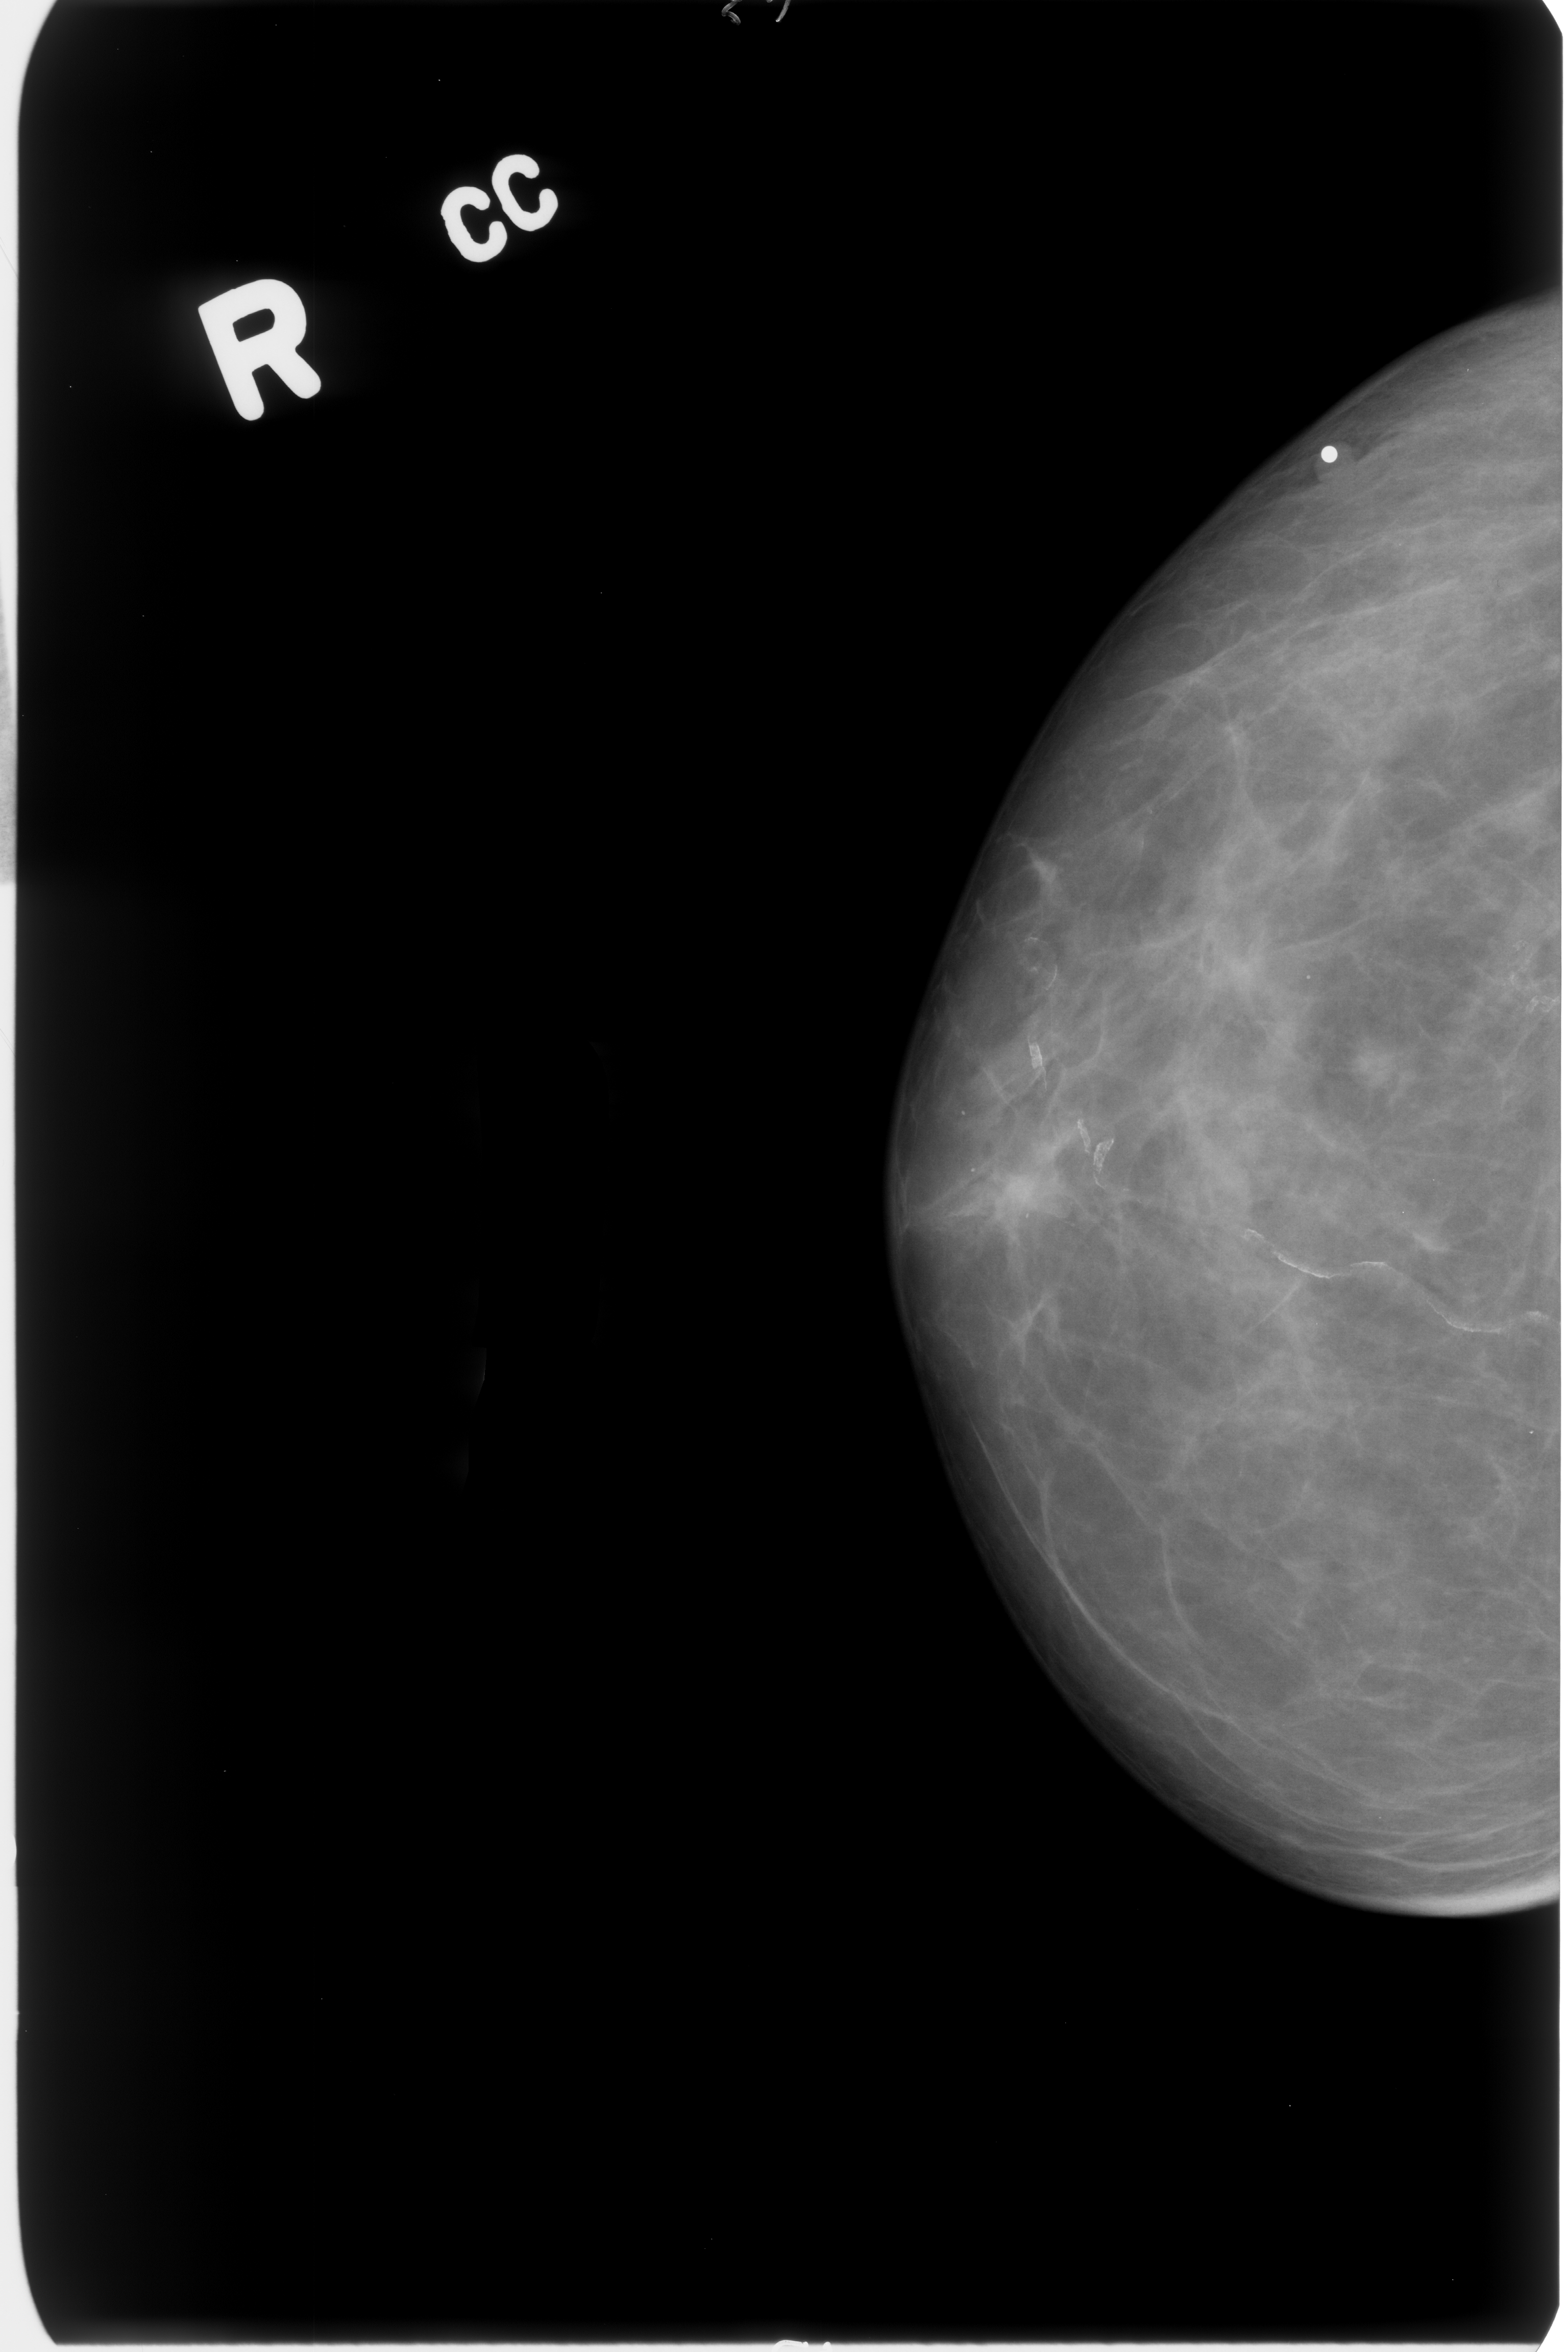
Scanned film-screen mammogram. Right breast. CC view. BI-RADS breast density category 2 (scale 1–4). 1568 × 2352 image matrix.
Expert-marked regions of interest on this image (one box per marked abnormality):
- calcifications, morphology vascular; BI-RADS assessment category 2; outcome (as recorded, no biopsy): benign without callback (not worked up further): bounding box (x1, y1, x2, y2) in pixels: (1033, 1110, 1561, 1344)